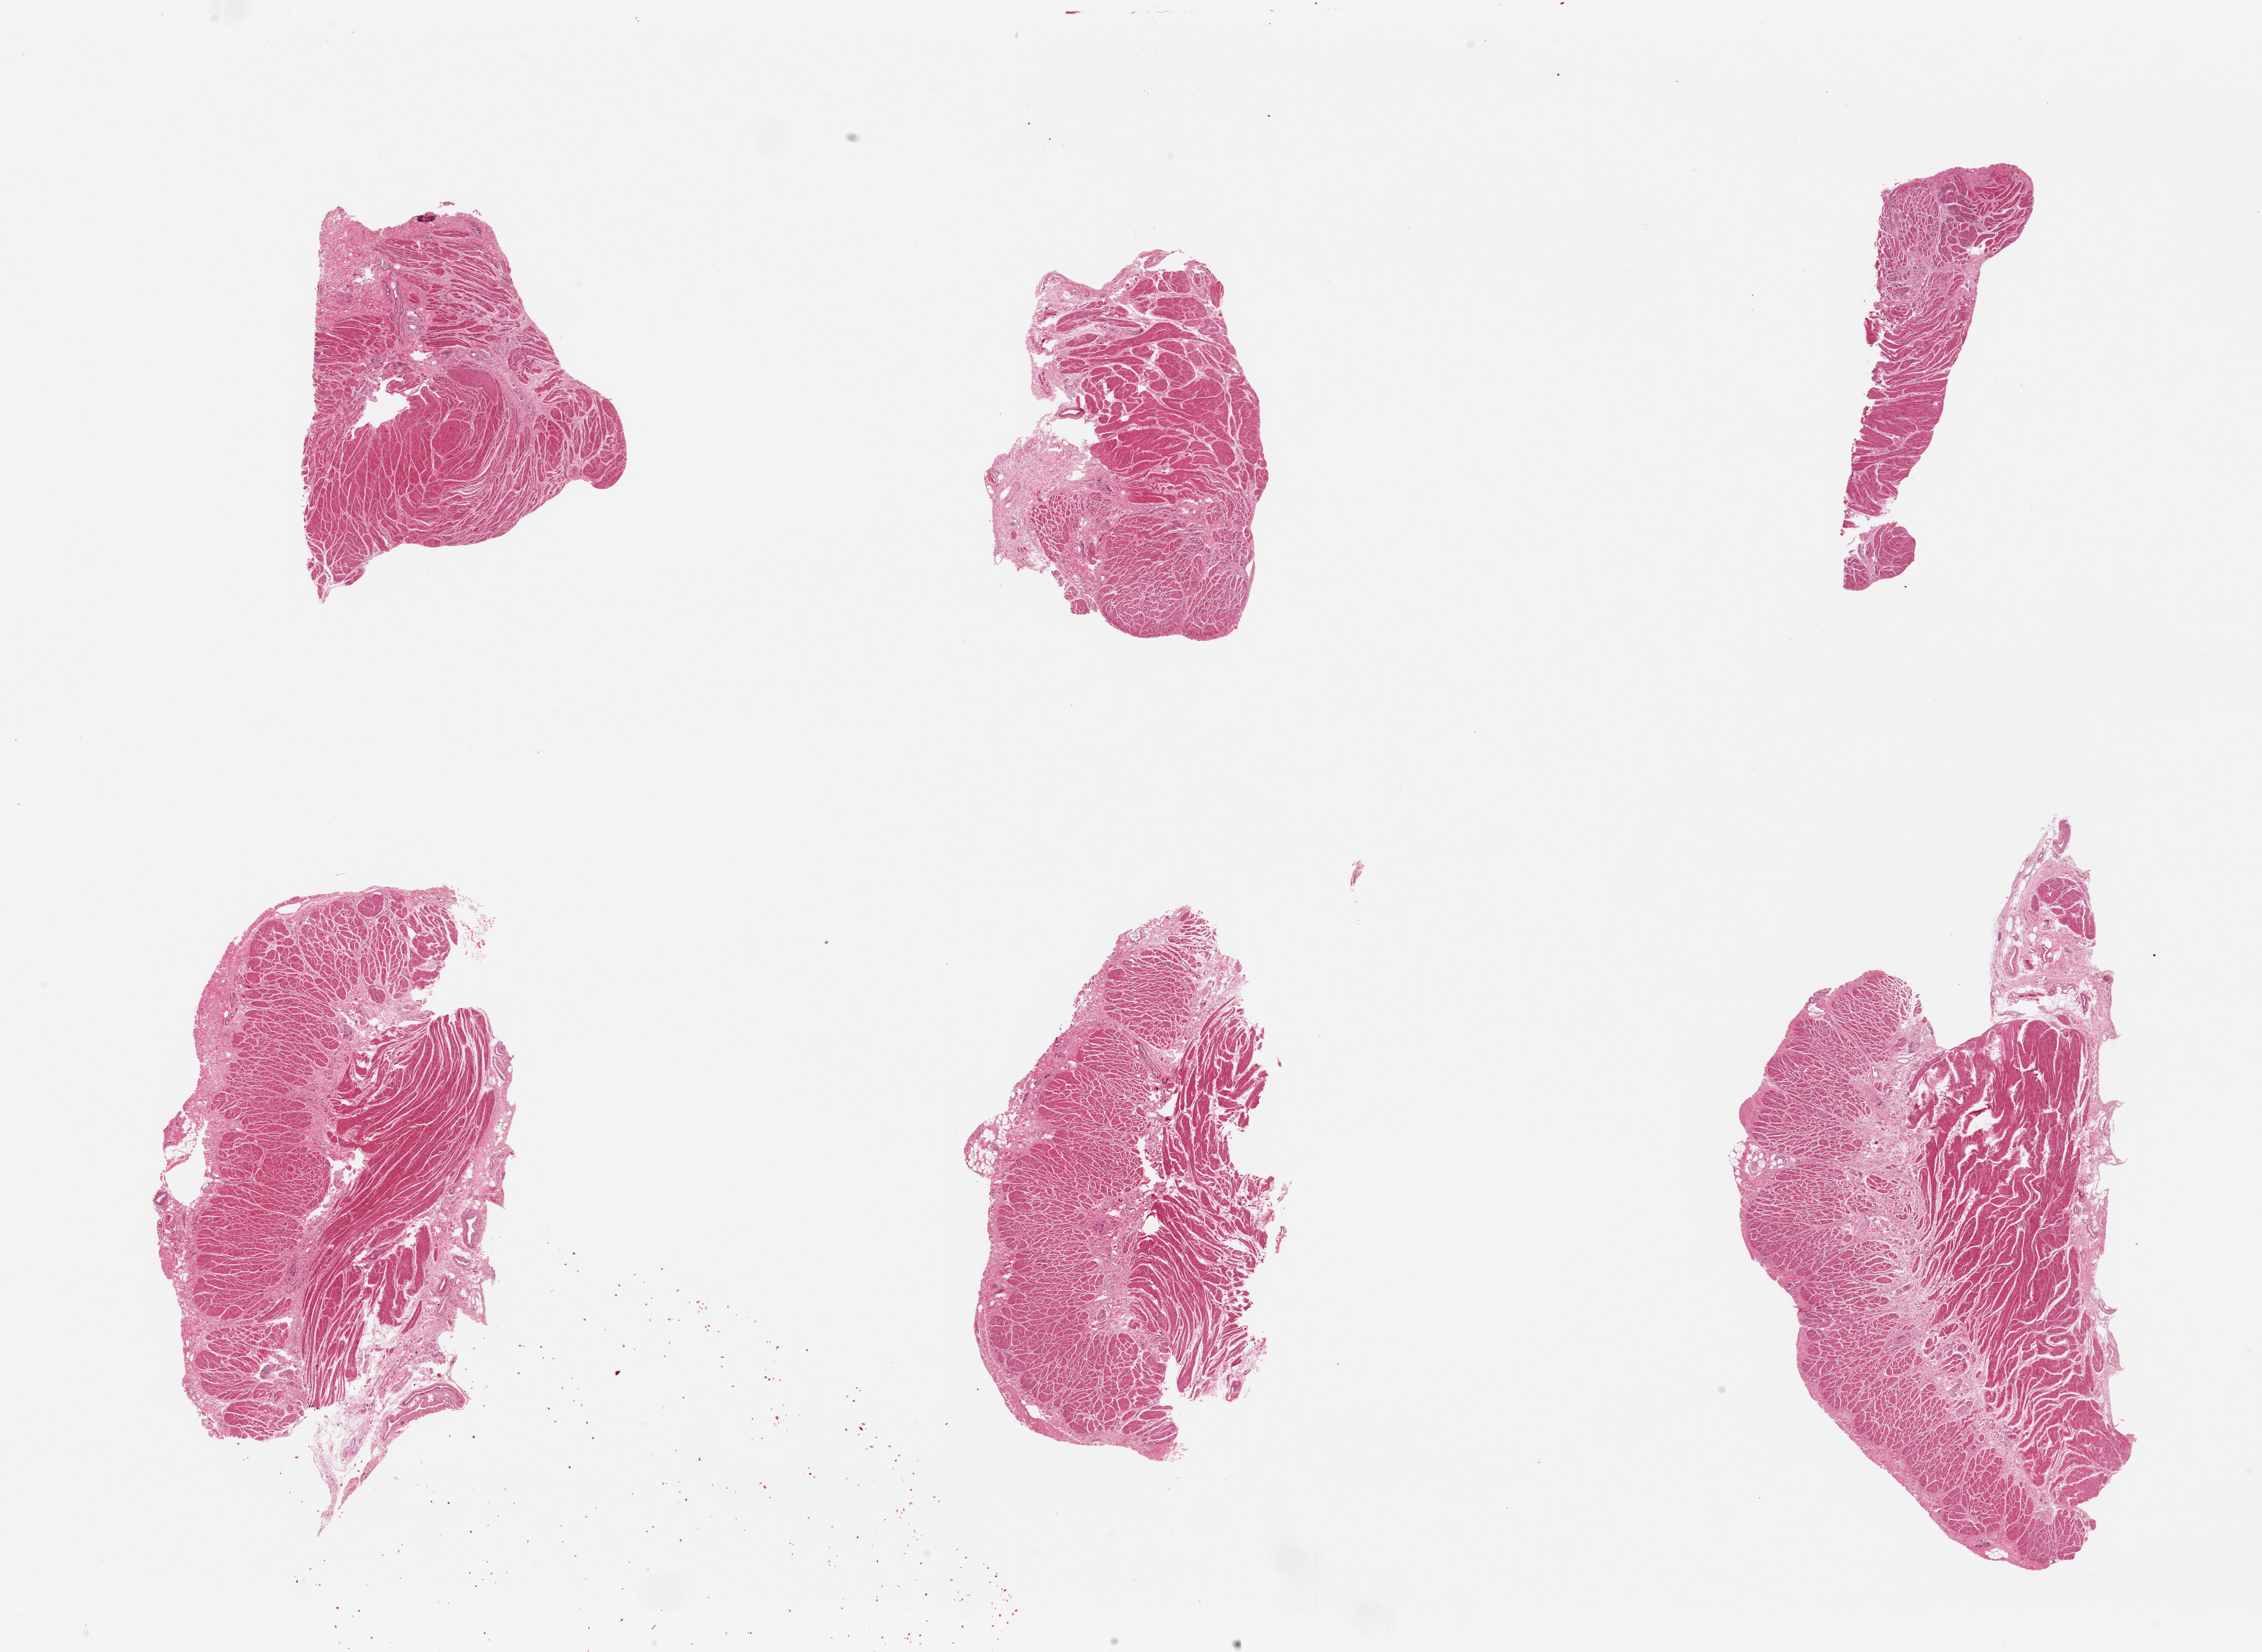
Whole-slide image, H&E stain, brightfield, a low-resolution overview of the entire scanned area, about 30.5 x 22.3 mm (slide scanned at 20x); PAXgene-fixed paraffin-embedded (PFPE) section; section of gastroesophageal junction (target tissue); tissue donor sample.
Reviewer comment on this tissue sample: 6 pieces, up to 10x5mm; all with (target) muscle.